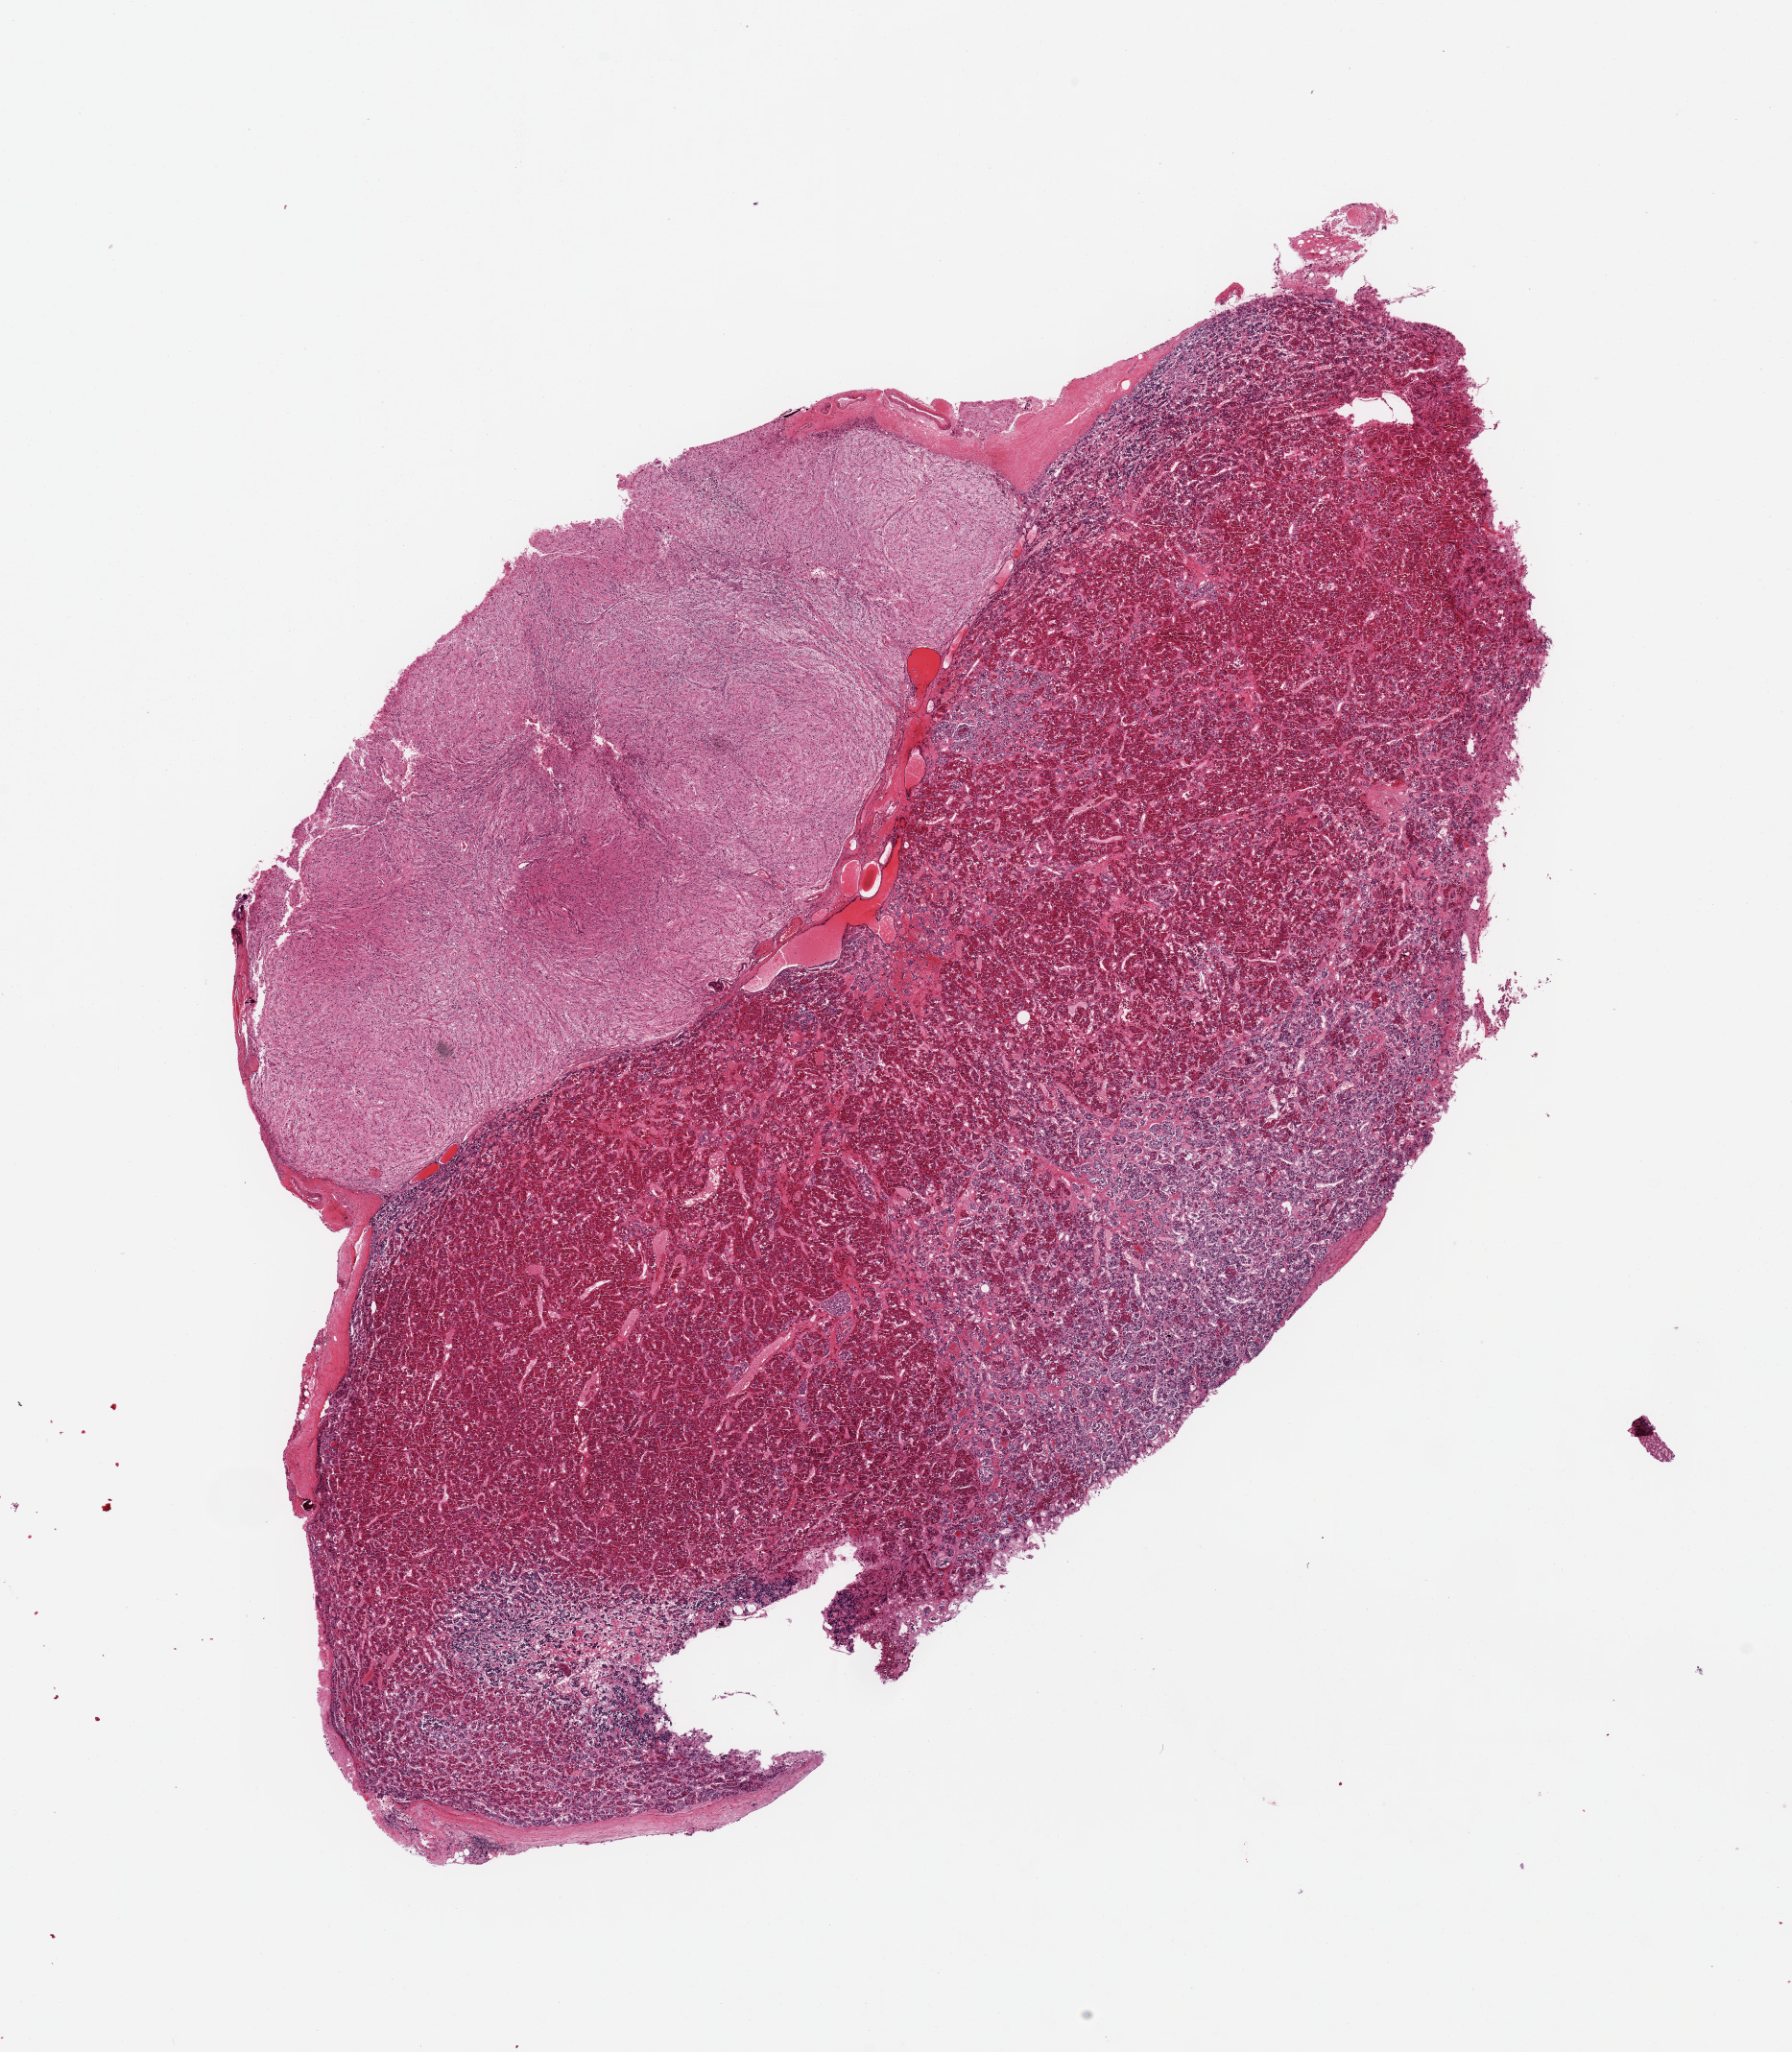
Whole-slide image, H&E stain, low-resolution overview of the scanned area, about 14.8 x 16.9 mm (from a 20x scan), PAXgene-fixed, paraffin-embedded tissue, sampled site (target tissue): pituitary, tissue donor sample. Donor sex: male.
Reviewer comment on this tissue sample: 1 piece; adenohypophysis and neurohypophysis.